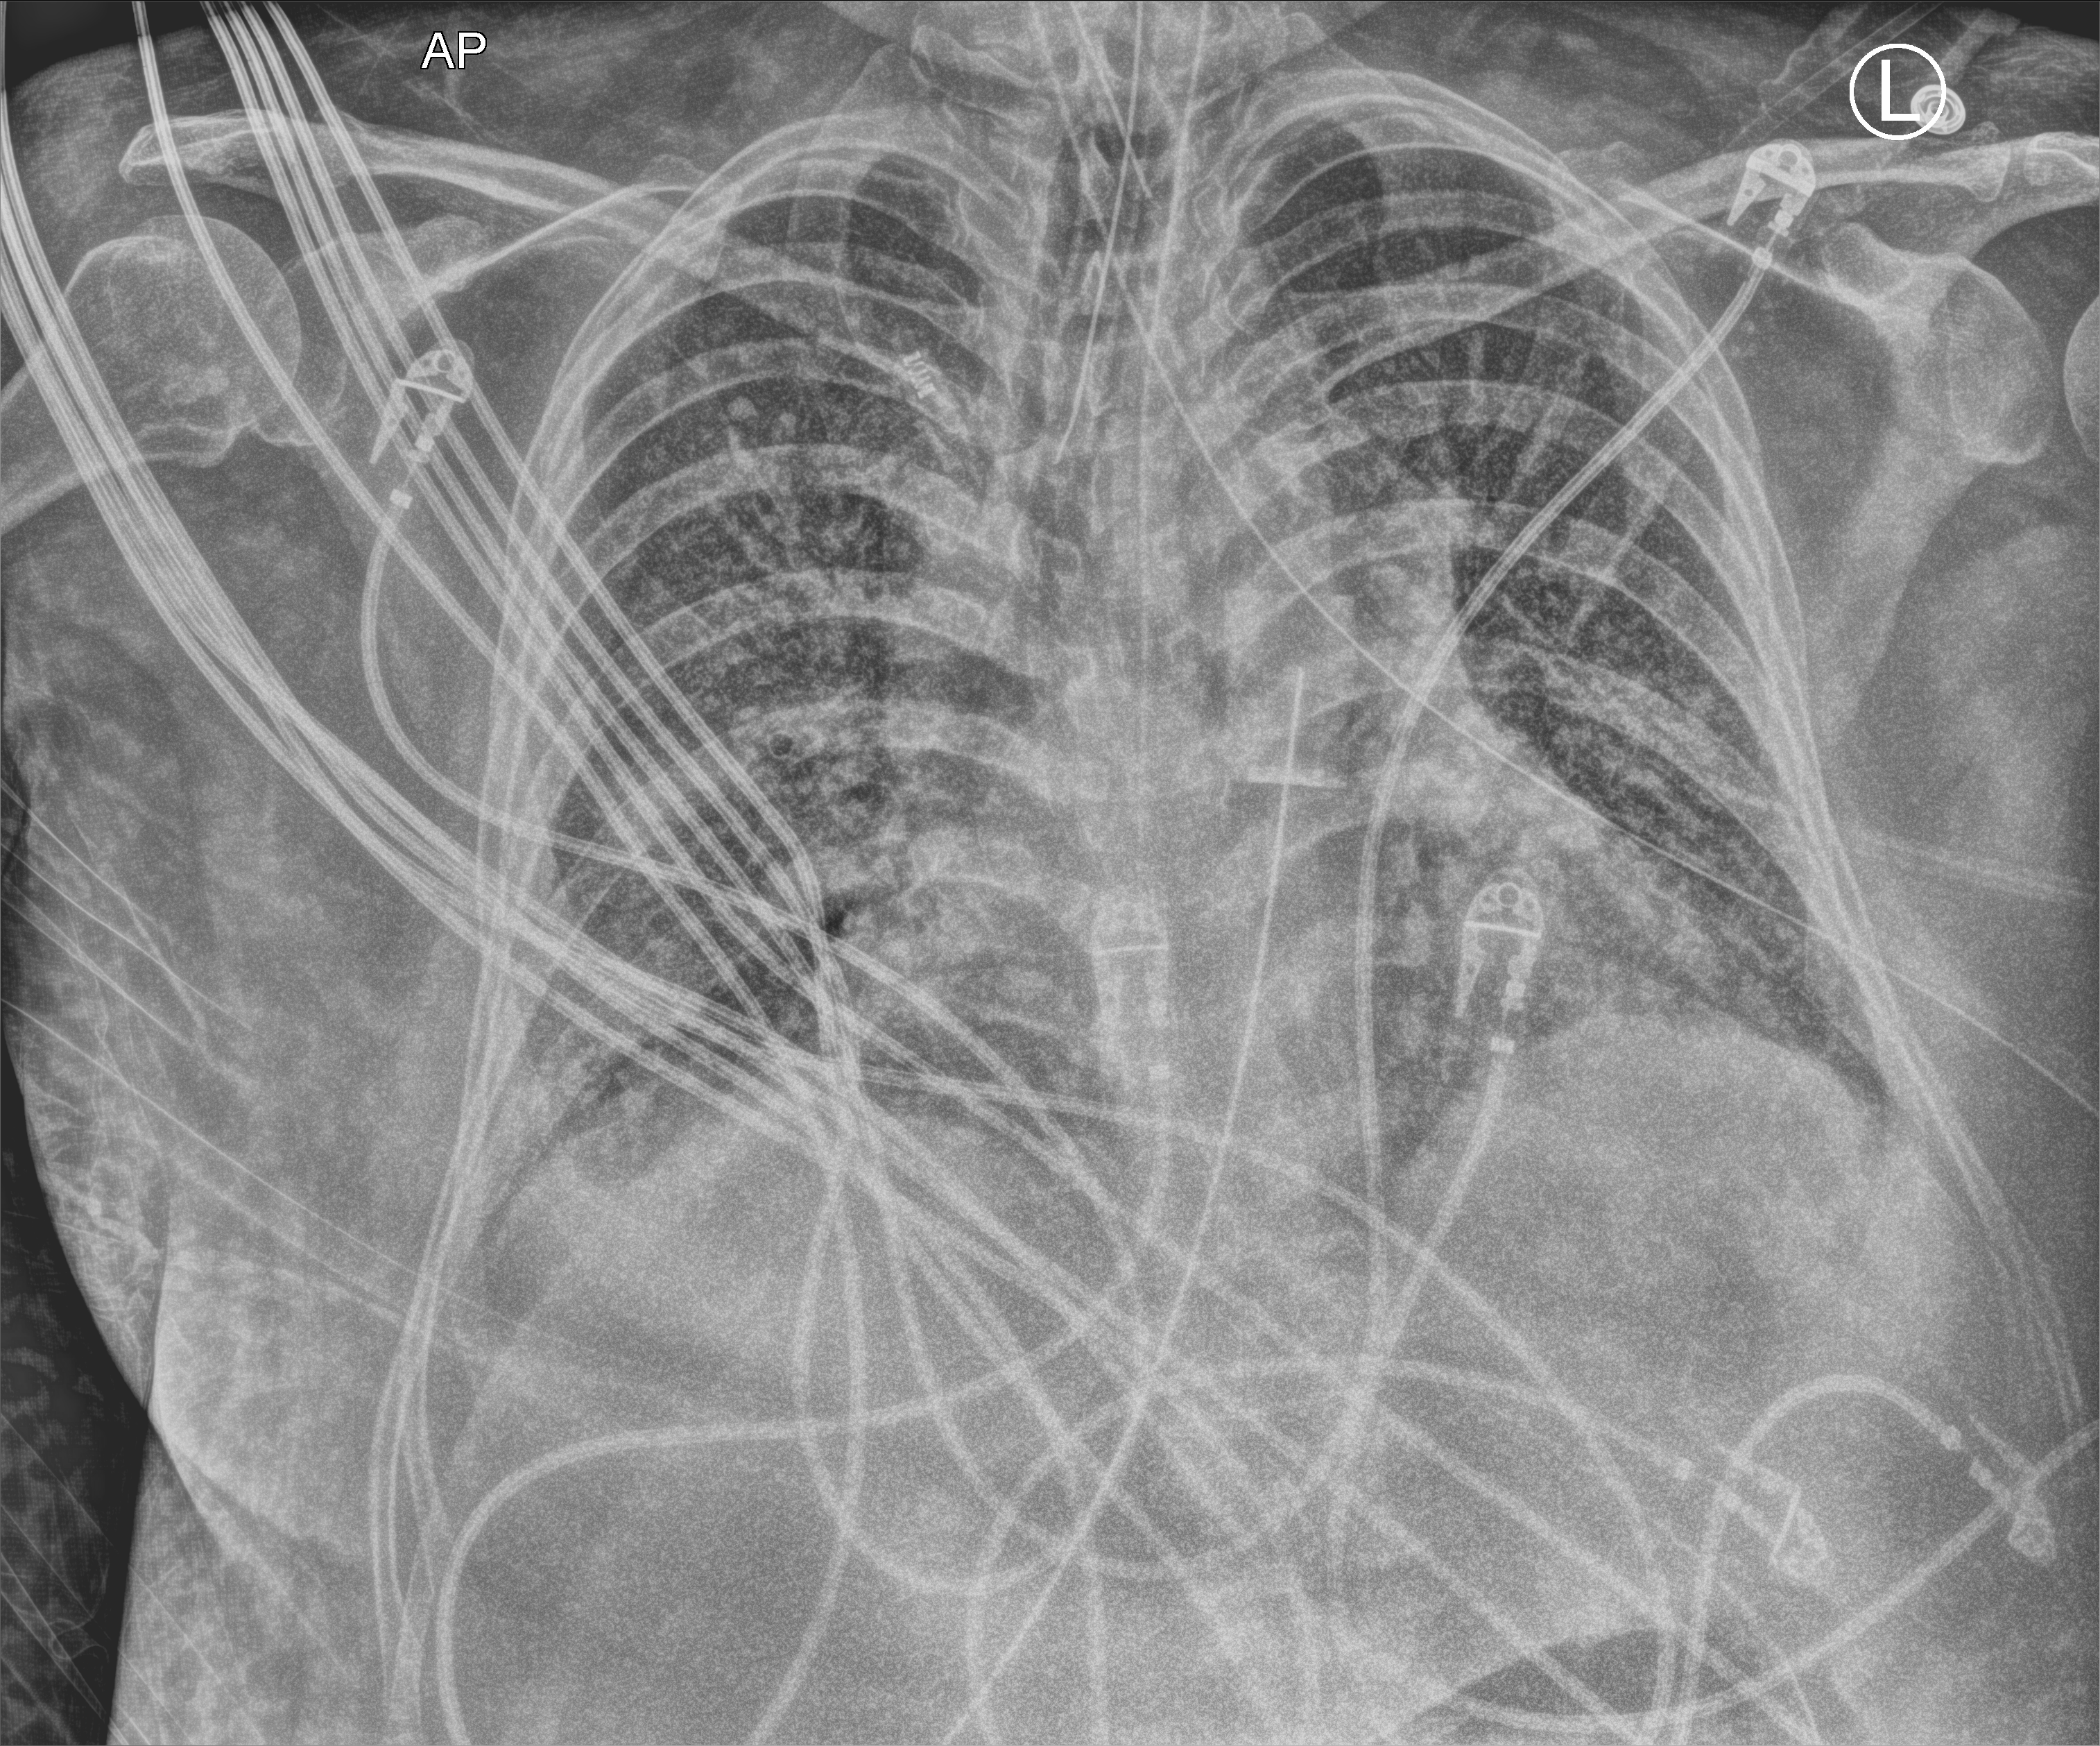
Portable chest radiograph, anteroposterior (AP) projection. Patient hospitalised with COVID-19, aged 18–59 years.
From the hospital-stay record, not from the radiograph (when in the stay this image was taken is not recorded): admitted to intensive care during this hospital stay: yes.